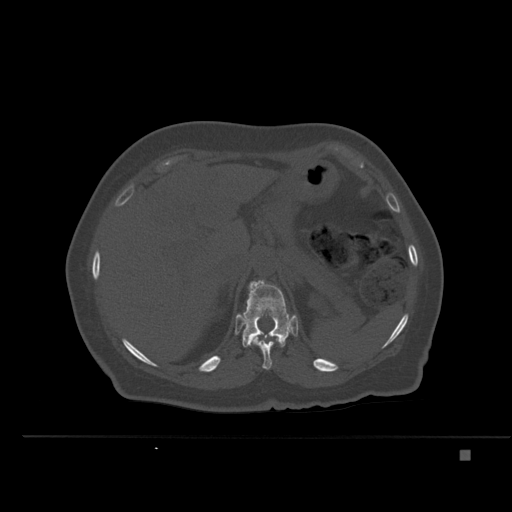
CT including the spine, one axial slice; slice 258 of 477 in the series (ordered by position); bone window (W 1800 / L 400 HU); 512 × 512 image matrix. Patient: female, 74 years. From the clinical record (not read from this slice): primary cancer: colon.
Structures marked on this image (semi-automatic segmentation, software-assisted and operator-edited):
- T11 vertebra: bounding box <251,336,284,369> (left, top, right, bottom; pixels)
- T12 vertebra: <242,280,292,347>